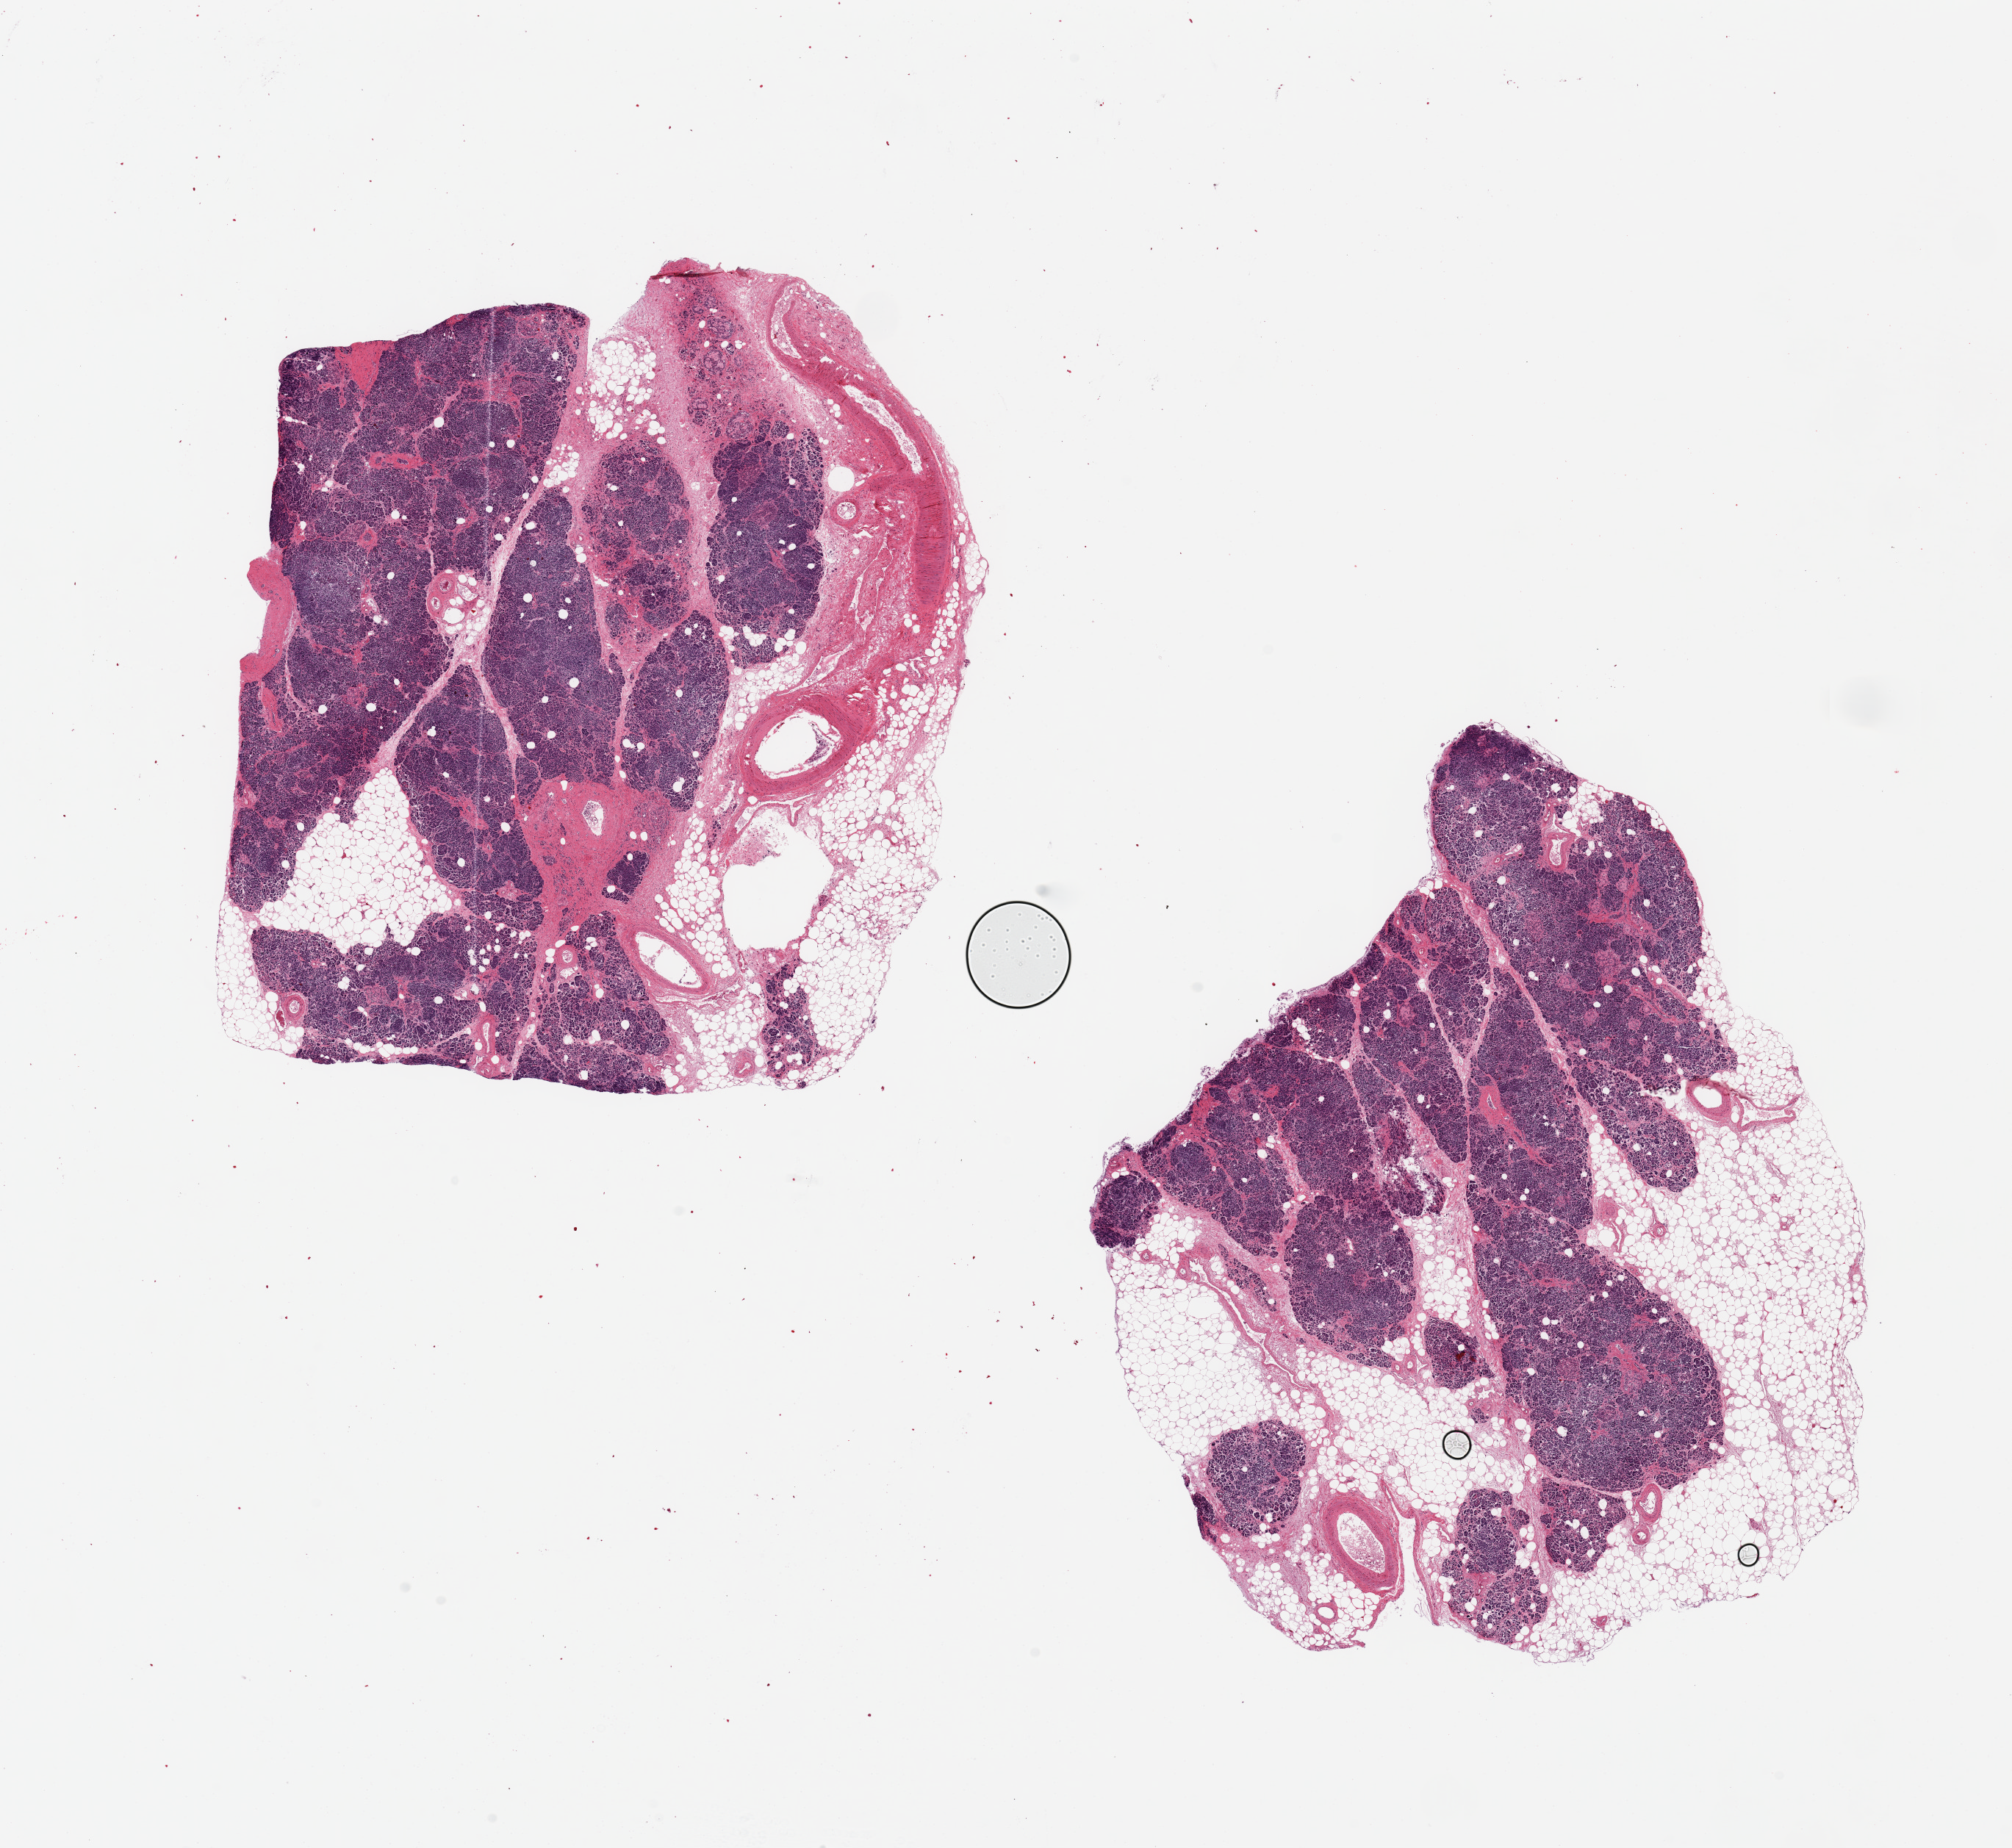
H&E whole-slide image — shown as a low-resolution overview of the whole scanned area (about 21.7 x 19.9 mm), PAXgene-fixed paraffin-embedded (PFPE) section, target tissue: pancreas, donor tissue sample. Donor sex: female.
Pathologist's review note for this sample: 2 pieces, 8x7 & 9x7.5mm; ~40 and 50% admixture with adipose and connective tissue; focal scarring of exocrine tissue in one piece.